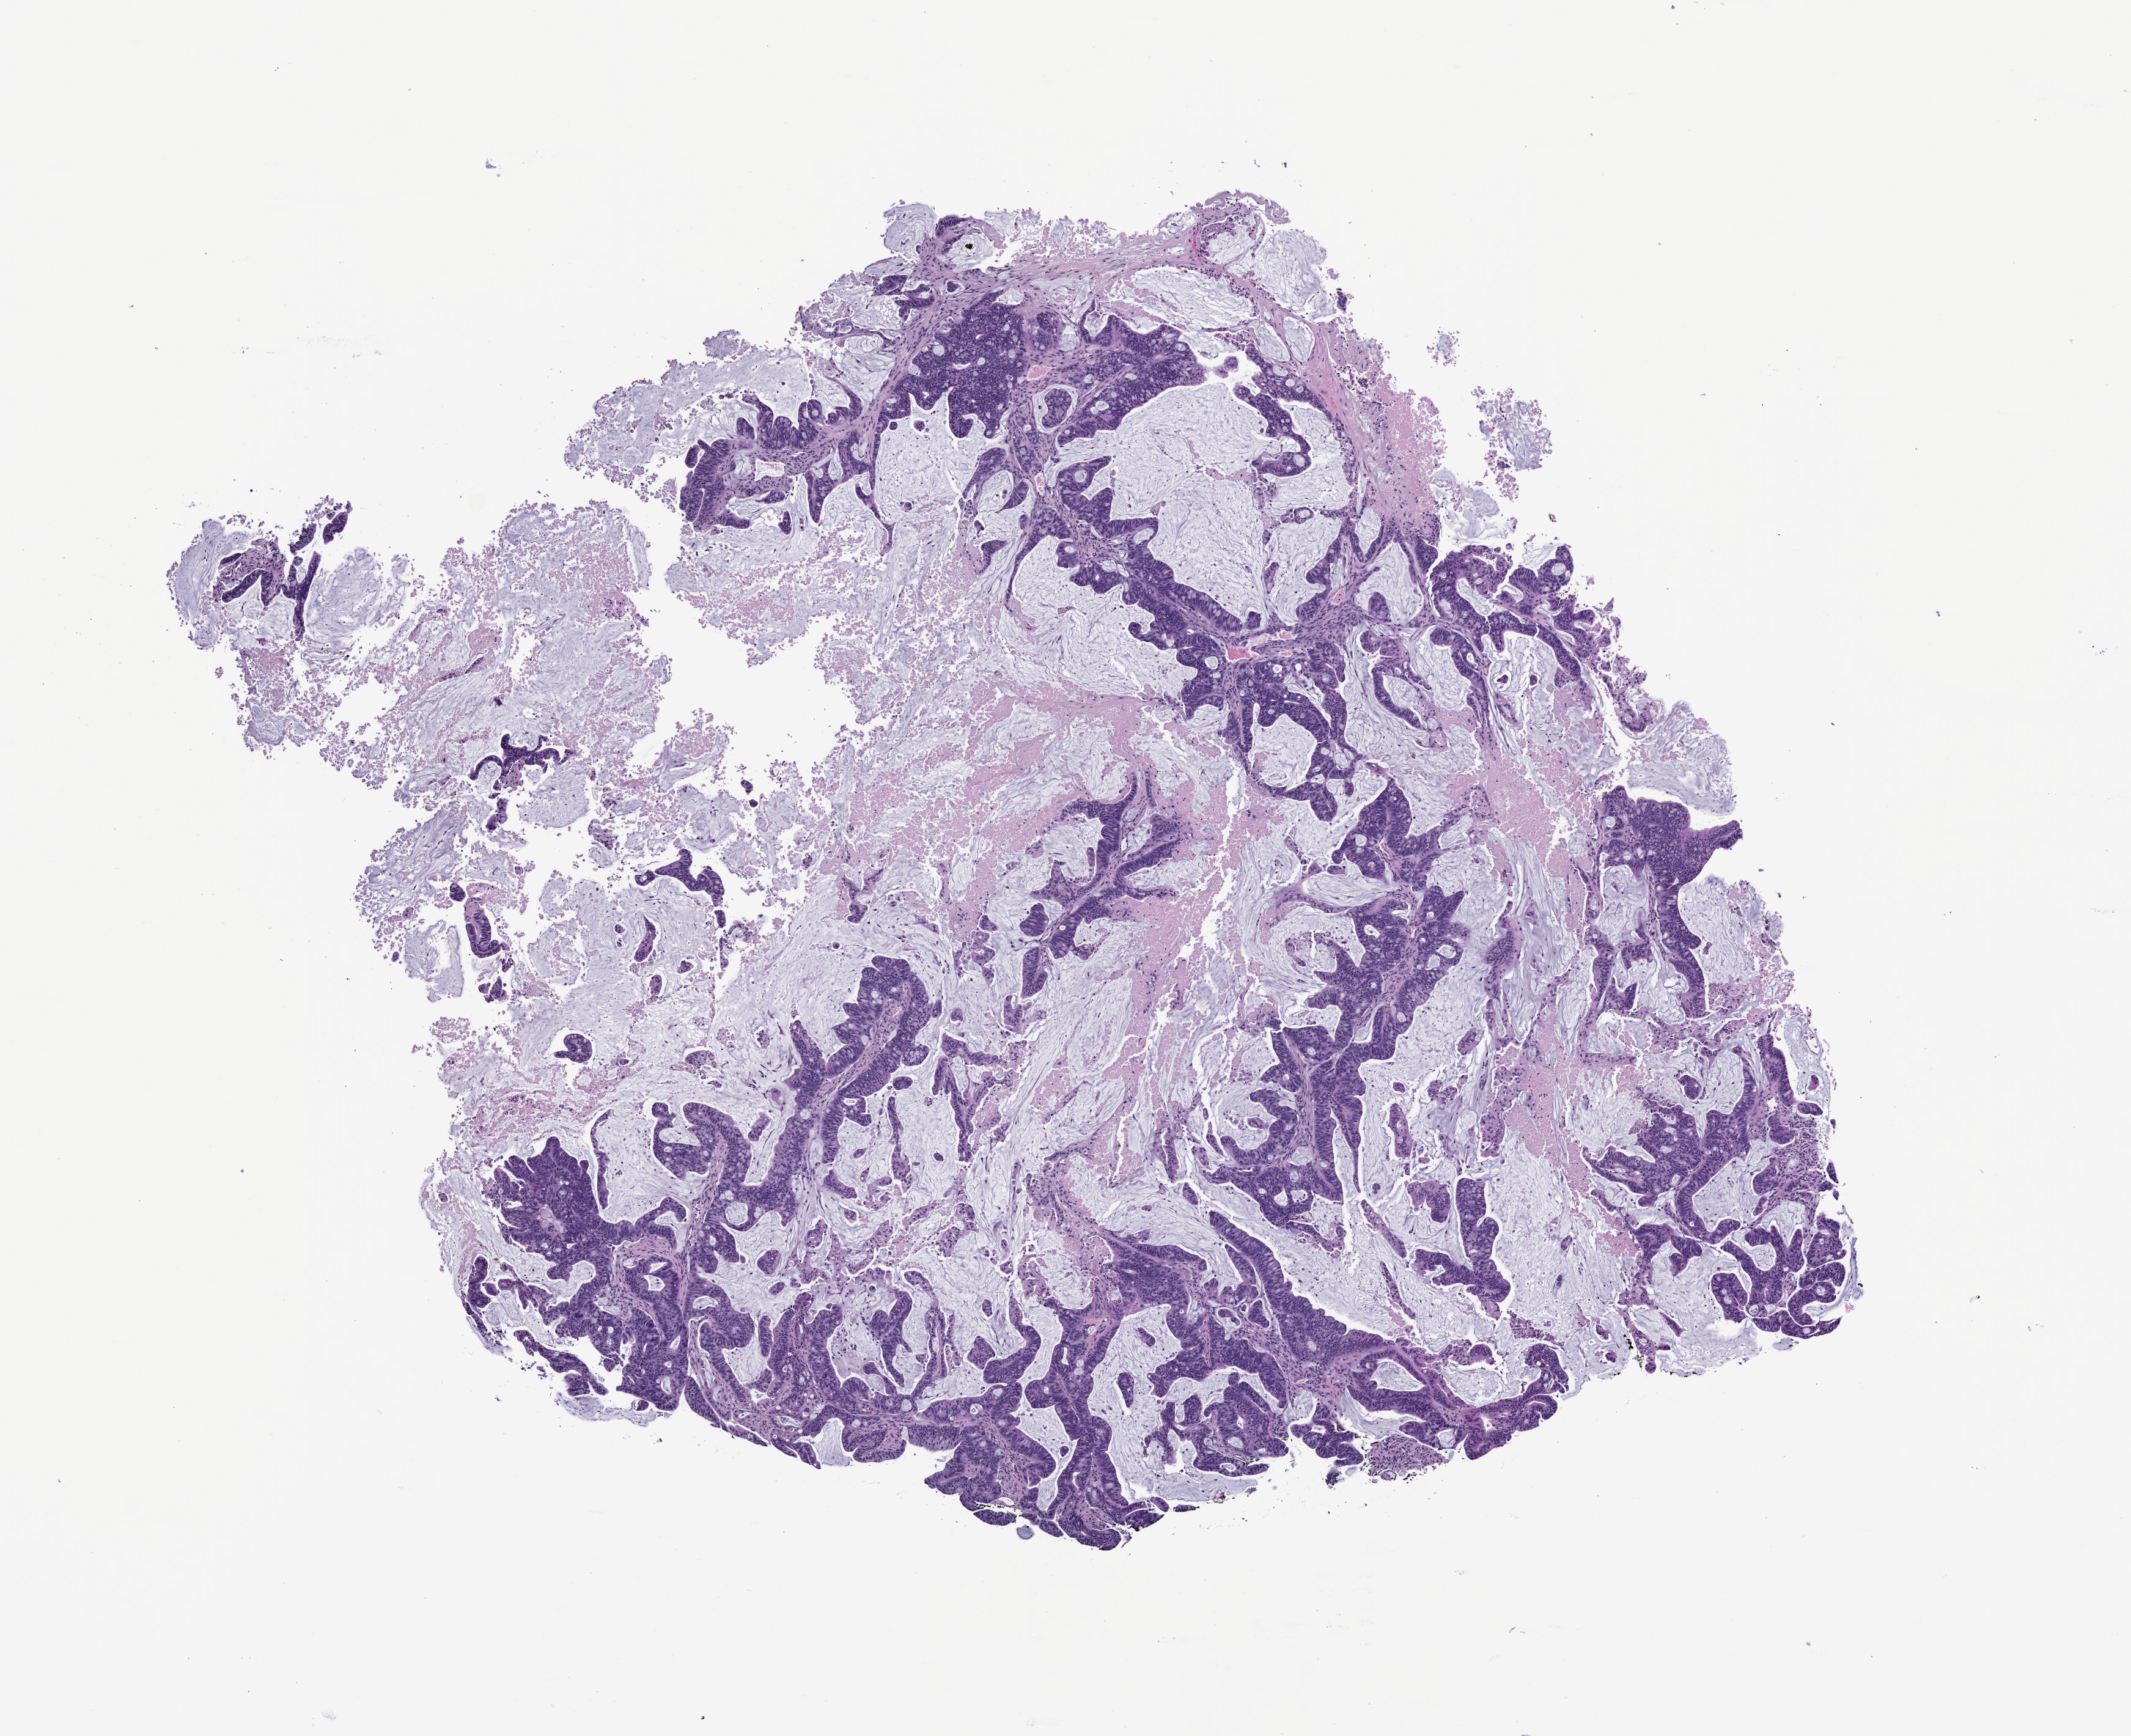
Haematoxylin and eosin whole-slide image of a patient-derived xenograft (PDX) tumor grown in a mouse, passage 1 — whole scanned area (about 7.0 x 5.7 mm) shown as a low-resolution overview; formalin-fixed paraffin-embedded section; originating tumor site category: rectum.
Originating patient diagnosis: Rectal Adenocarcinoma.